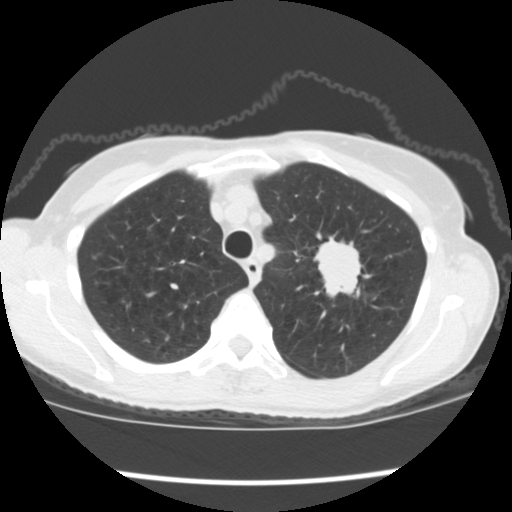
Low-dose screening chest CT, axial slice; first (baseline) screen; lung window (W 1500 / L -600 HU); 120 kVp; slice 33 of 176 in the series. Female, age 67 years at enrolment. Former smoker at enrolment.
- Expert reader's lesion annotation, box from (x=305, y=235) to (x=378, y=310) px.
- The exam's reader record, not a measurement of the box and not confirmed to be the same lesion: non-calcified nodule or mass ≥4 mm, left upper lobe, 34 × 32 mm, spiculated (stellate) margins, soft tissue attenuation, pre-existing on the prior screen: no.
- Official screen result: positive, change unspecified: nodule(s) >= 4 mm or enlarging nodule(s), mass(es), or other non-specific abnormalities suspicious for lung cancer.
- Participant outcome: lung cancer diagnosed 17 days after this screen — small cell carcinoma, NOS, left upper lobe, stage IIIA (AJCC 6th edition), 40 mm at pathology.